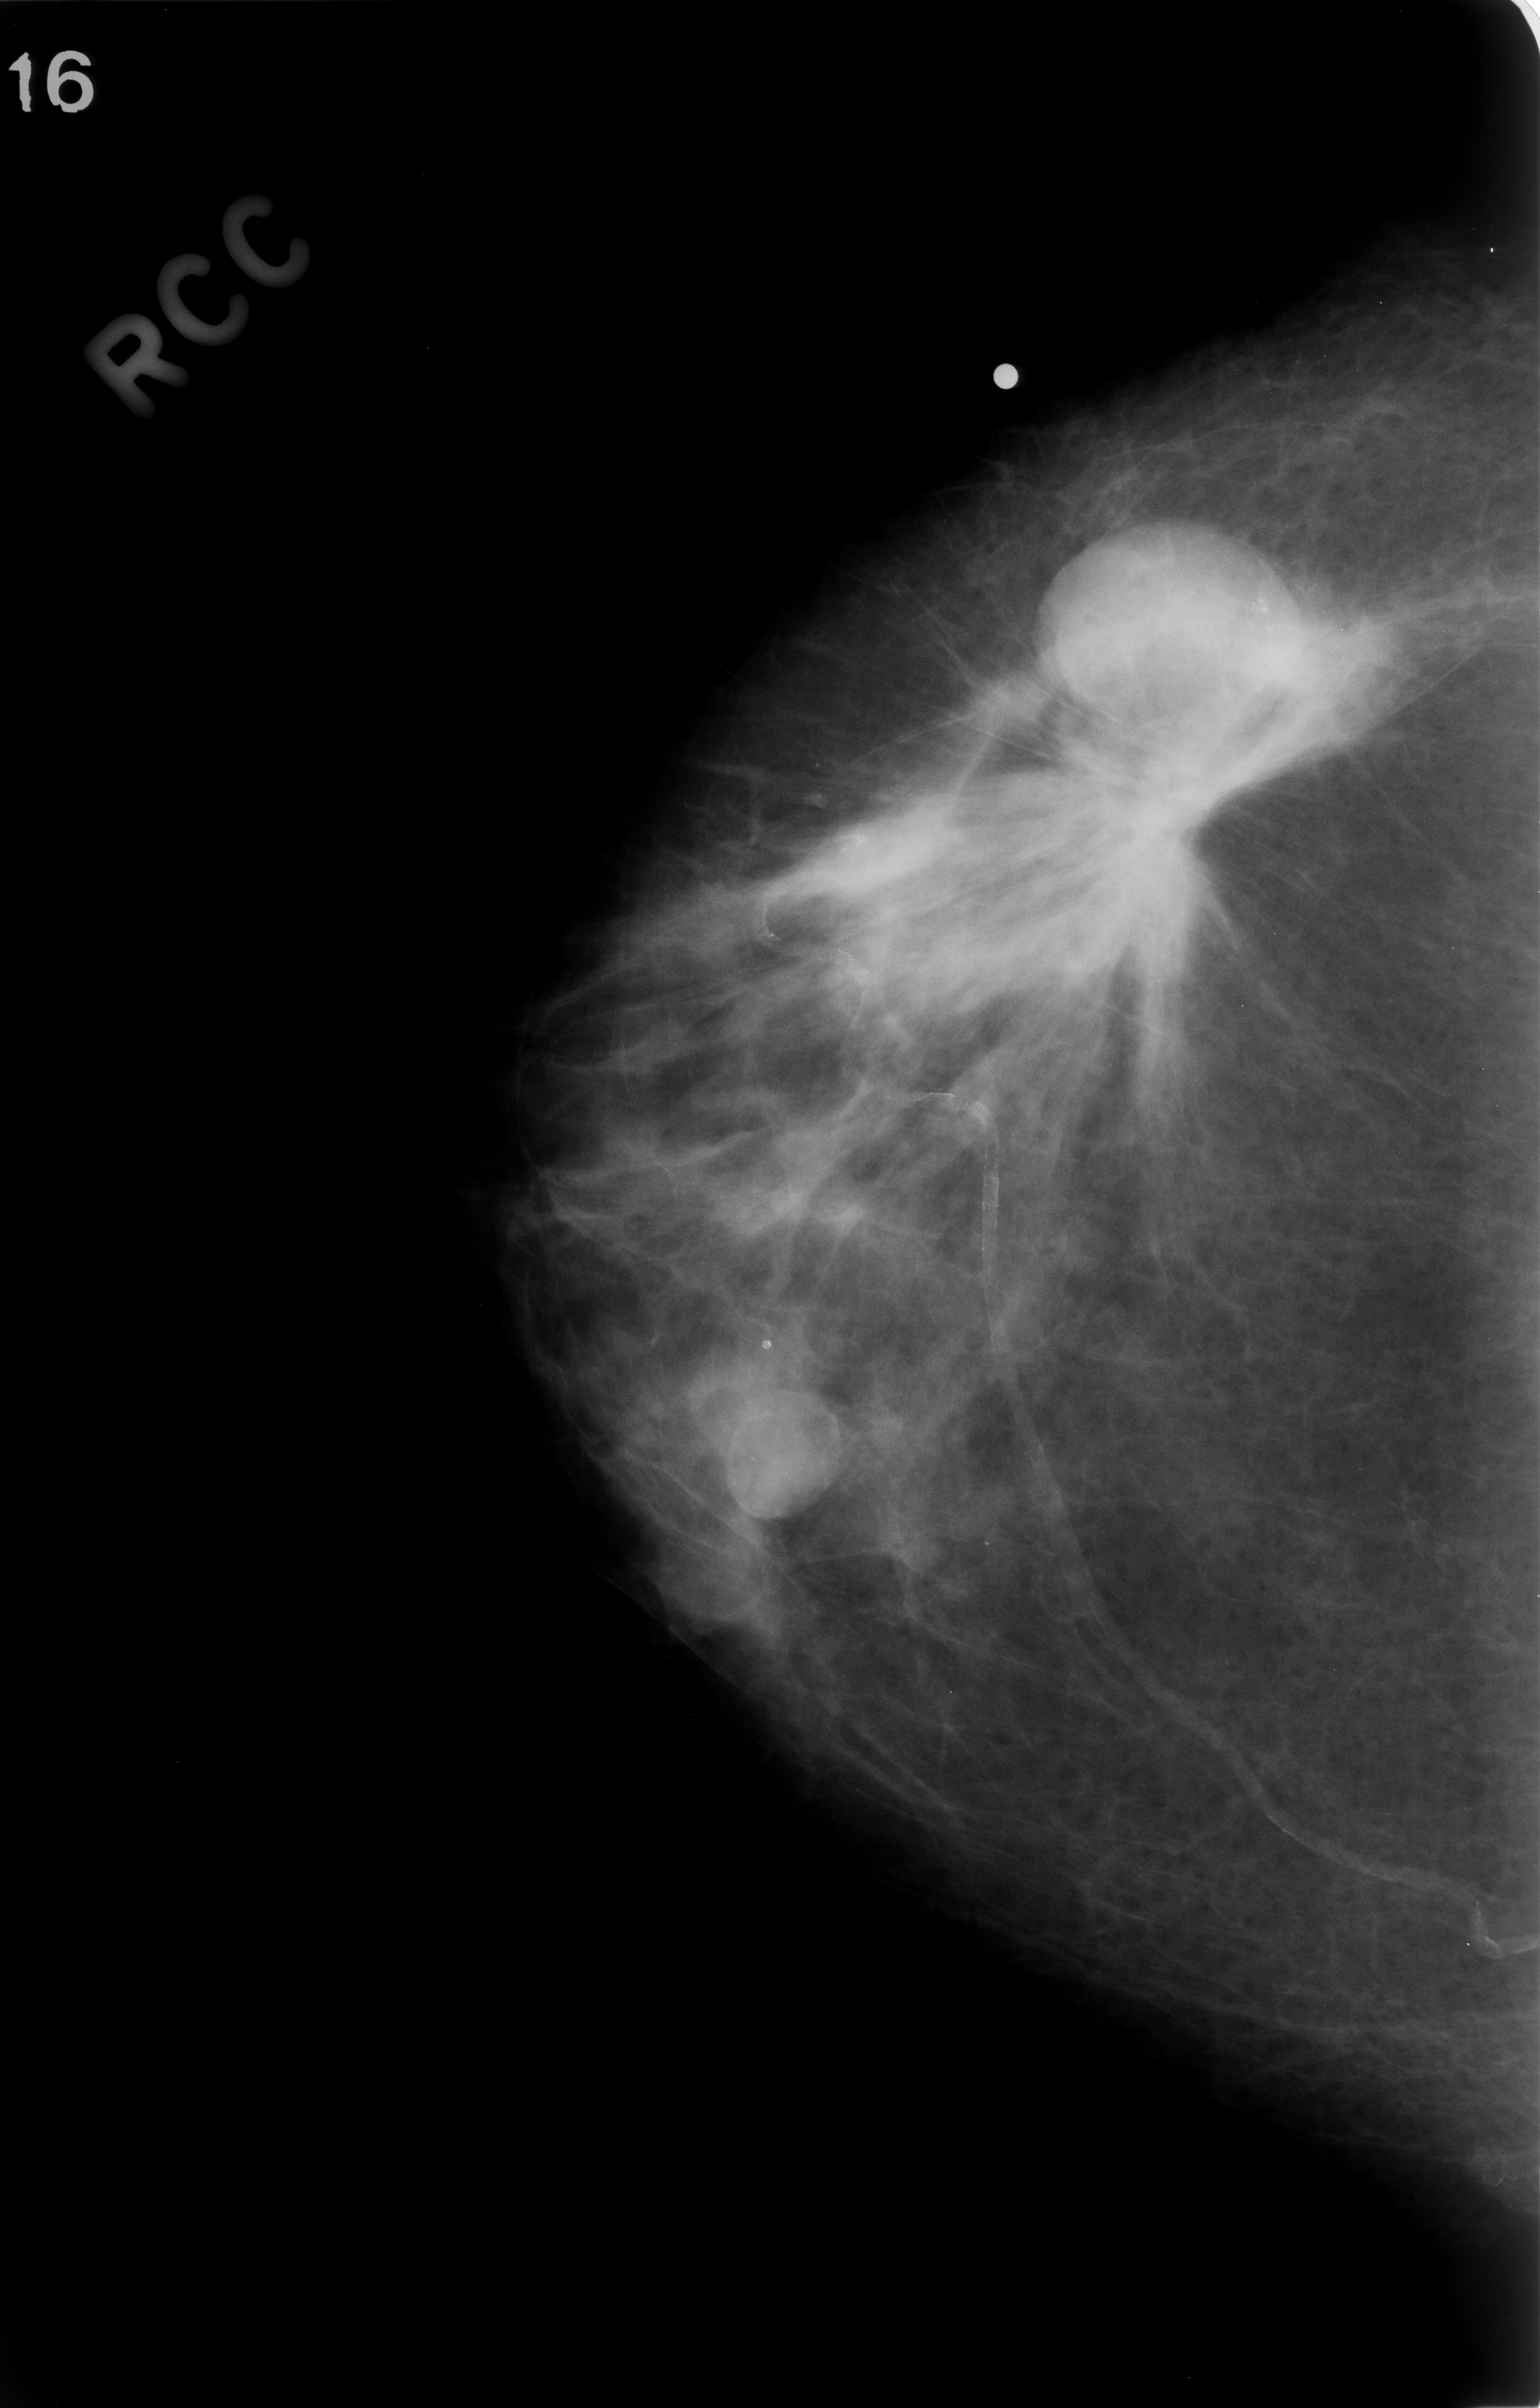
Mammogram (digitized film); right breast; CC view; breast composition: scattered fibroglandular densities (BI-RADS density category 2 of 4).
Marked findings (only marked abnormalities are described; nothing is implied about the rest of the image): mass, shape irregular, margins spiculated; BI-RADS assessment category 5; pathology (as recorded): malignant.